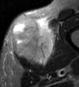
MRI of an extremity soft-tissue mass, one axial slice; slice 17 of 45 in the series (ordered by position); STIR; MR volume resampled by the dataset authors to the PET/CT grid (not the native acquisition matrix); 3.27 mm slice thickness; 79 × 87 image matrix, field of view 77 × 85 mm. Male patient. From the clinical record (not read from this slice): histological type: pleiomorphic leiomyosarcoma; grade: high; site of the primary tumour: left thigh.
Outlined on this slice (expert contour drawn on MRI and transferred to this co-registered scan by the dataset authors):
- gross tumour volume including surrounding oedema: bounding box (x1, y1, x2, y2) in pixels: (11, 18, 58, 65)
- gross tumour volume (mass): (11, 18, 55, 65)